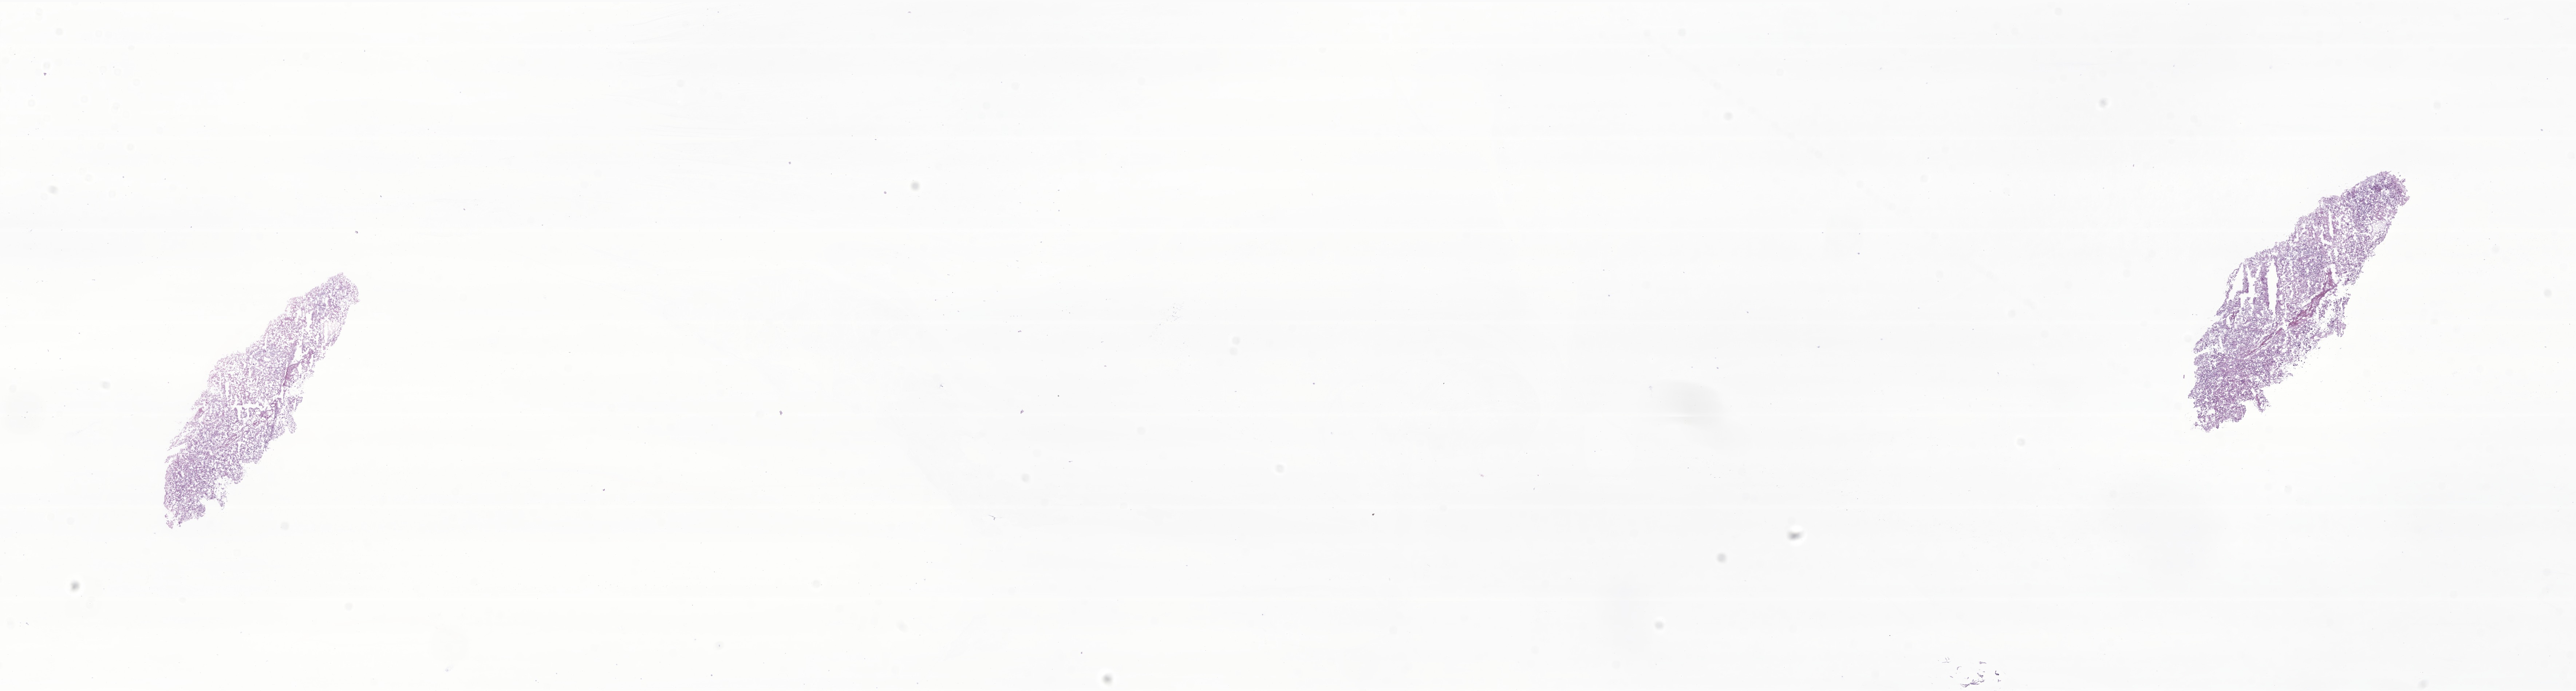
Whole-slide image, hematoxylin and eosin (H&E) stain of tumor tissue from the brain — a low-resolution overview of the entire scanned area, about 29.8 x 8.0 mm; frozen section (OCT-embedded). Patient female; age 48 months.
Diagnosis (ICD-O-3 morphology term): Neoplasm, malignant.